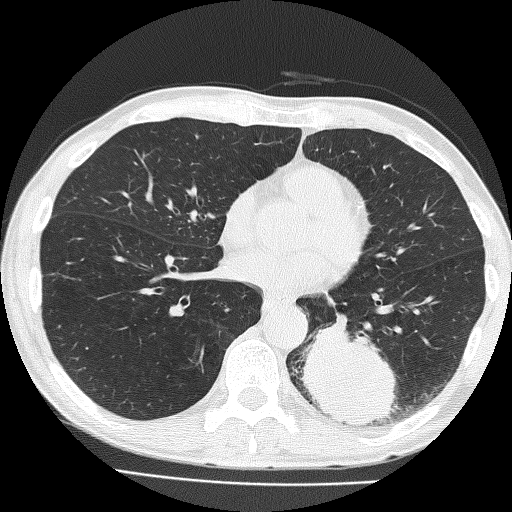
Axial slice from a low-dose chest CT screening exam, baseline annual screen, lung window (W 1500 / L -600 HU), lung (sharp) reconstruction kernel (FC51), 512 × 512 image matrix. Male participant, aged 58 years at enrolment. Current smoker at enrolment.
• Expert-annotated lung lesion, bounding box (x1, y1, x2, y2) in pixels: (300, 310, 421, 434).
• The screening reader recorded 2 non-calcified nodules or masses ≥4 mm on this exam (left lower lobe, left upper lobe); which of them this box marks is not recorded.
• Official screen result: positive, change unspecified: nodule(s) >= 4 mm or enlarging nodule(s), mass(es), or other non-specific abnormalities suspicious for lung cancer.
• Participant outcome: lung cancer diagnosed 39 days after this screen — non-small cell carcinoma, left lower lobe, poorly differentiated (G3), stage IV (AJCC 6th edition), 74 mm at pathology.